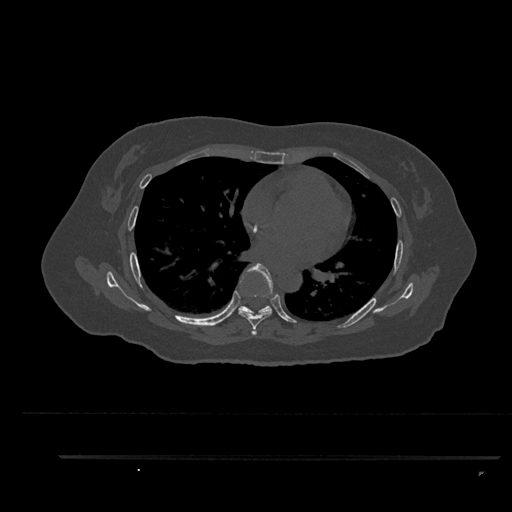
CT including the spine, one axial slice. Bone window (W 1800 / L 400 HU). 0.5 mm slice thickness. 512 × 512 image matrix, field of view 408 × 408 mm. Female patient, age 44 years. Case-level facts recorded for this patient, not image findings: primary cancer: renal; vertebrae with lytic lesions (as recorded): L1.
Annotated regions visible in this slice (semi-automatic segmentation, software-assisted and operator-edited):
- T6 vertebra: box from (x=238, y=263) to (x=273, y=335) px
- T7 vertebra: (x=238, y=305)–(x=272, y=315)